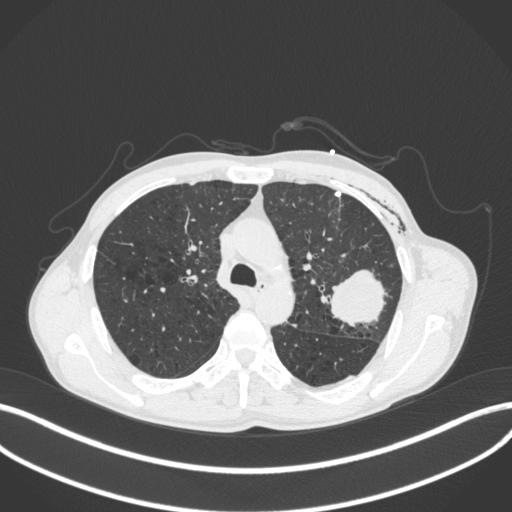
Chest CT, one axial slice. Position 278 of 416 along the scan axis. Reconstruction kernel B31f. 120 kVp. Lung window (W 1500 / L -600 HU). 512 × 512 image matrix. Patient: male, 58 years. From the clinical record (not read from this slice): clinical TNM (as recorded): T3 N0 M0.
Structures marked on this image (rectangle marked by the reading radiologist):
- lung tumour (recorded histology: adenocarcinoma): bounding box <319,262,394,328> (left, top, right, bottom; pixels)